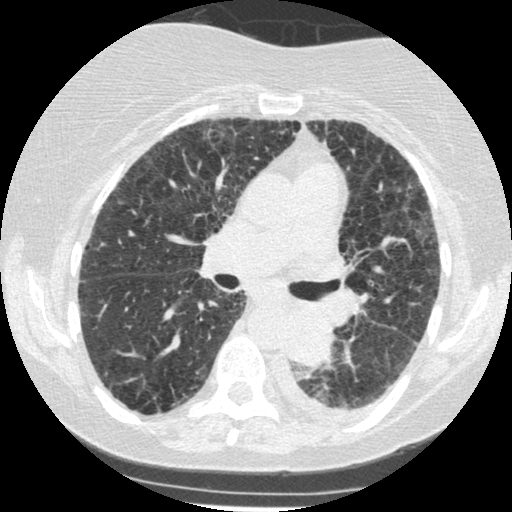
Low-dose screening chest CT, one axial slice; position 148 of 341 along the scan axis; 120 kVp; lung window (W 1500 / L -600 HU); 1.25 mm slice thickness; 512 × 512 image matrix, field of view 310 × 310 mm.
Structures marked on this image (expert manual segmentation):
- lesion 1 (tumor, lower lobe of left lung): bounding box <286,309,335,367> (left, top, right, bottom; pixels)